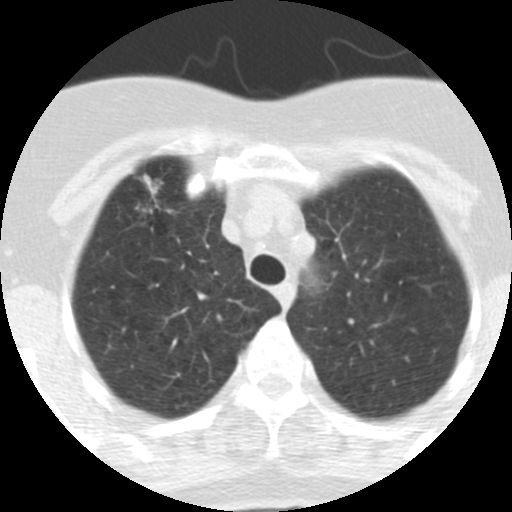
Low-dose screening chest CT, one axial slice; slice 253 of 313 in the series (ordered by position); lung window (W 1500 / L -600 HU); 2.5 mm slice thickness; 512 × 512 image matrix, field of view 253 × 253 mm.
Structures marked on this image (outlined manually by an expert reader):
- lesion 1 (tumor, upper lobe of right lung): box from (x=143, y=175) to (x=163, y=198) px